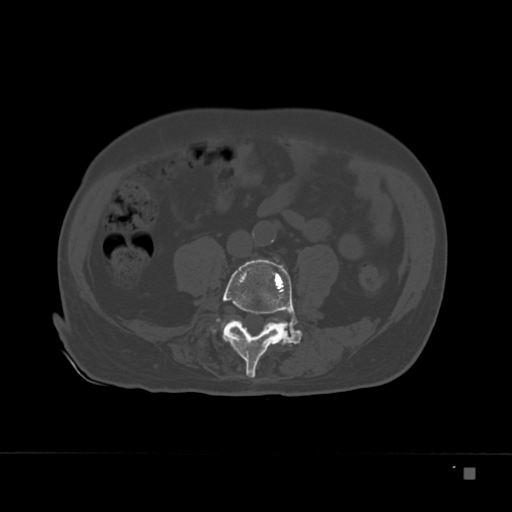
CT including the spine, one axial slice; slice 42 of 332 in the series (ordered by position); reconstruction kernel Br40s; 120 kVp; bone window (W 1800 / L 400 HU); 1.5 mm slice thickness; 512 × 512 image matrix. Patient: male, 72 years. Case-level facts recorded for this patient, not image findings: primary cancer: skeletal.
Outlined on this slice (semi-automatically segmented with operator editing):
- L4 vertebra: bounding box <216,259,302,378> (left, top, right, bottom; pixels)
- L5 vertebra: <217,321,224,326>